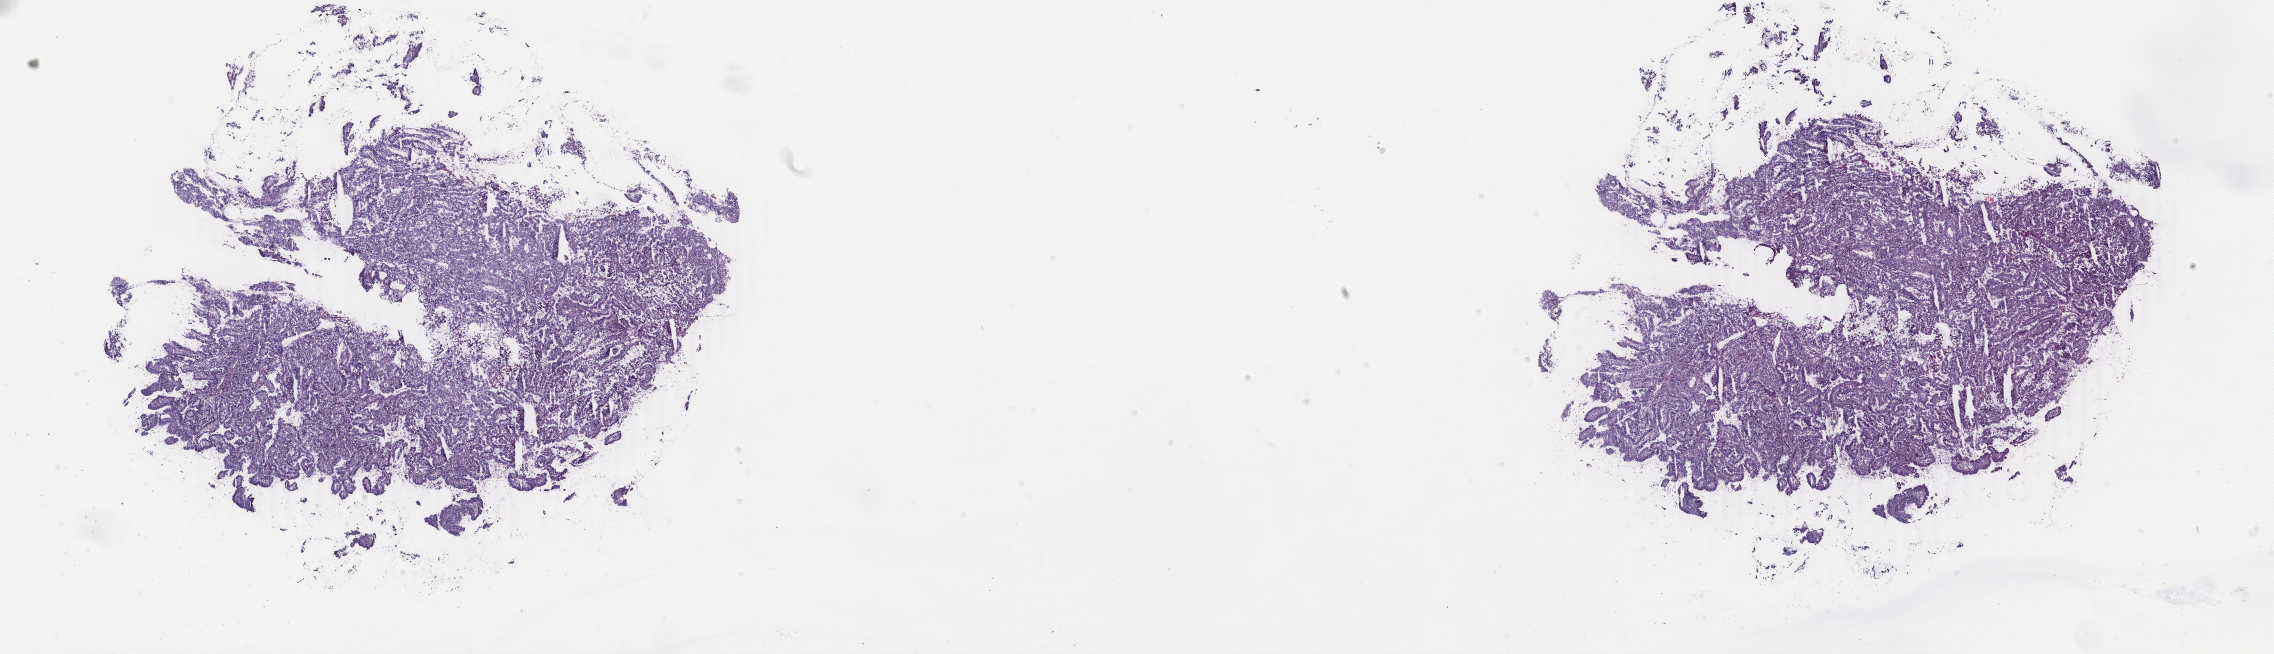
Digitized Hematoxylin and eosin (H&E) stained tissue section (whole slide), whole scanned area (about 36.2 x 10.4 mm, from a 40x scan) shown as a low-resolution overview; frozen section from the top of the tissue portion; uterus, primary tumour sample. Female patient. Composition of this section per pathologist review: tumour cells 100%, tumour nuclei 90%.
Diagnosis: Serous cystadenocarcinoma, NOS (endometrium).